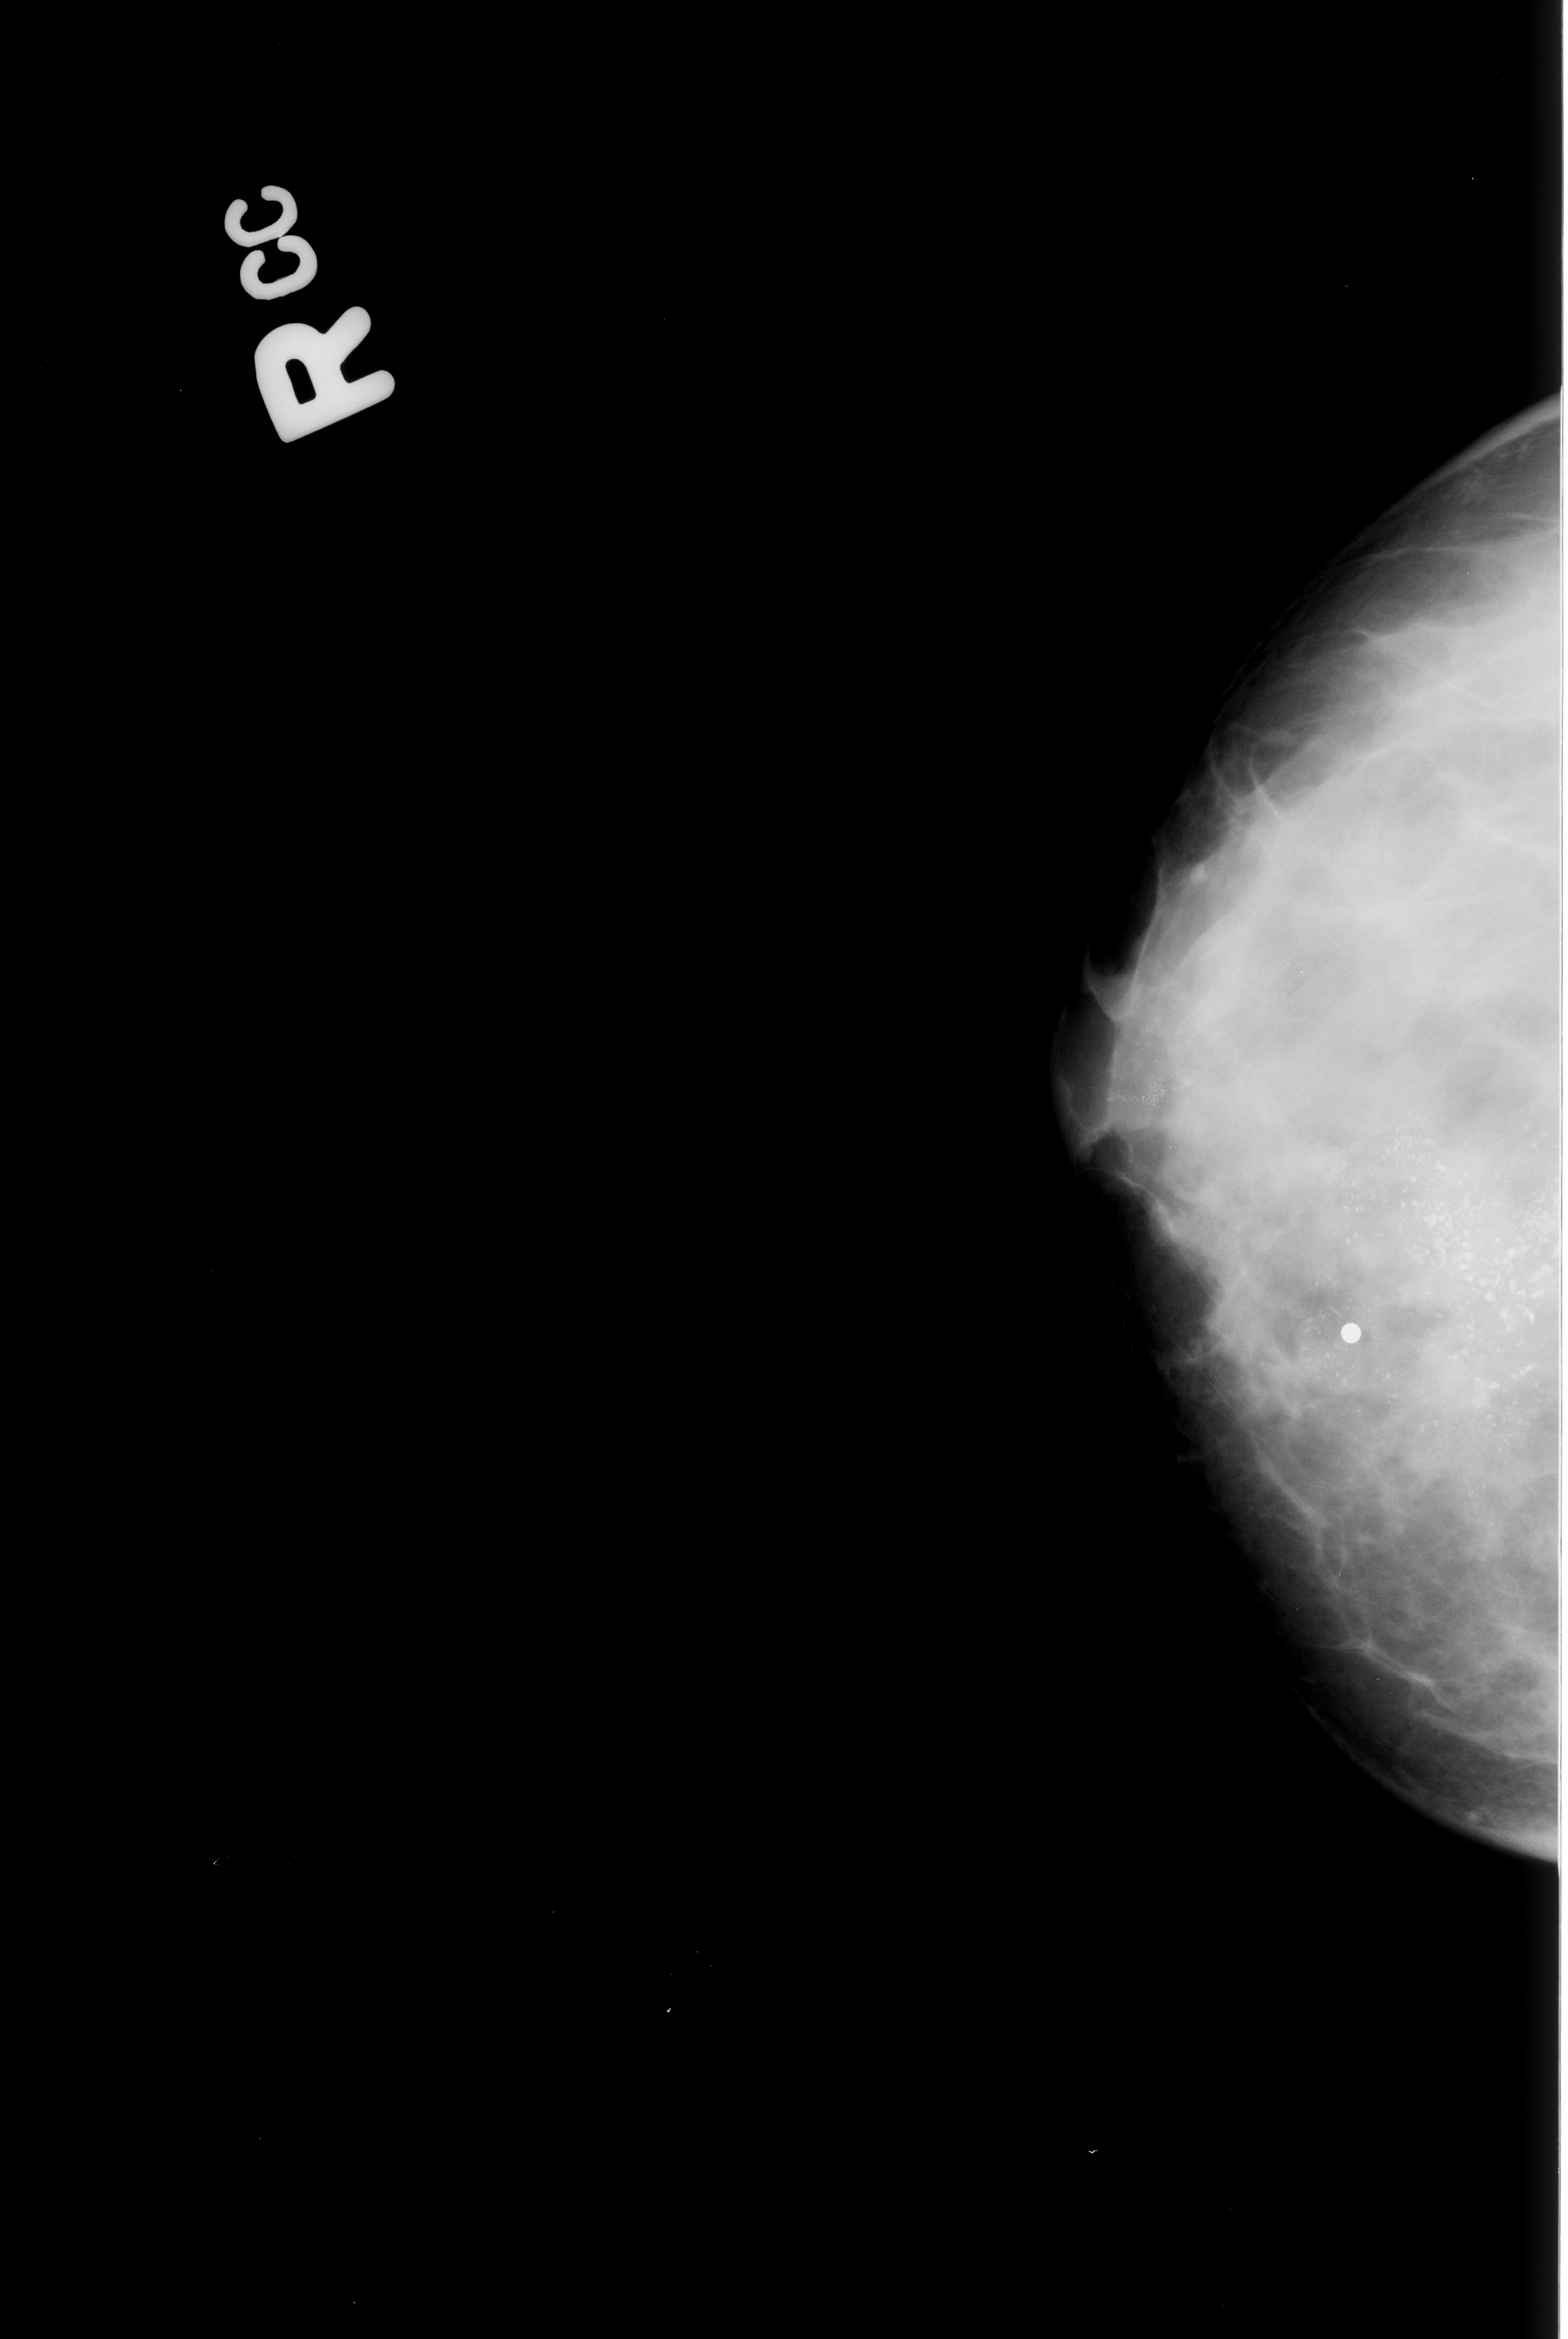
Mammogram (digitized film), right breast, CC view, BI-RADS breast density category 3 (scale 1–4).
Marked findings (only marked abnormalities are described; nothing is implied about the rest of the image): calcifications, morphology pleomorphic, distribution regional; BI-RADS assessment category 5; subtlety rating 5 on a 1 (subtle) to 5 (obvious) scale; pathology result (as recorded, not read from the image): malignant.